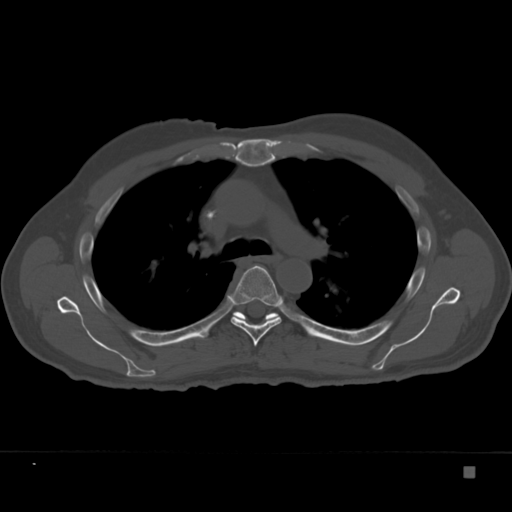
CT including the spine, one axial slice; position 253 of 332 along the scan axis; reconstruction kernel Br40s; bone window (W 1800 / L 400 HU); 1.5 mm slice thickness; 512 × 512 image matrix, field of view 389 × 389 mm. Male patient, age 72 years. From the clinical record (not read from this slice): primary cancer: skeletal.
Outlined on this slice (semi-automatically segmented with operator editing):
- T5 vertebra: bounding box [x1, y1, x2, y2] px = [228, 265, 283, 346]
- T6 vertebra: [232, 311, 280, 322]